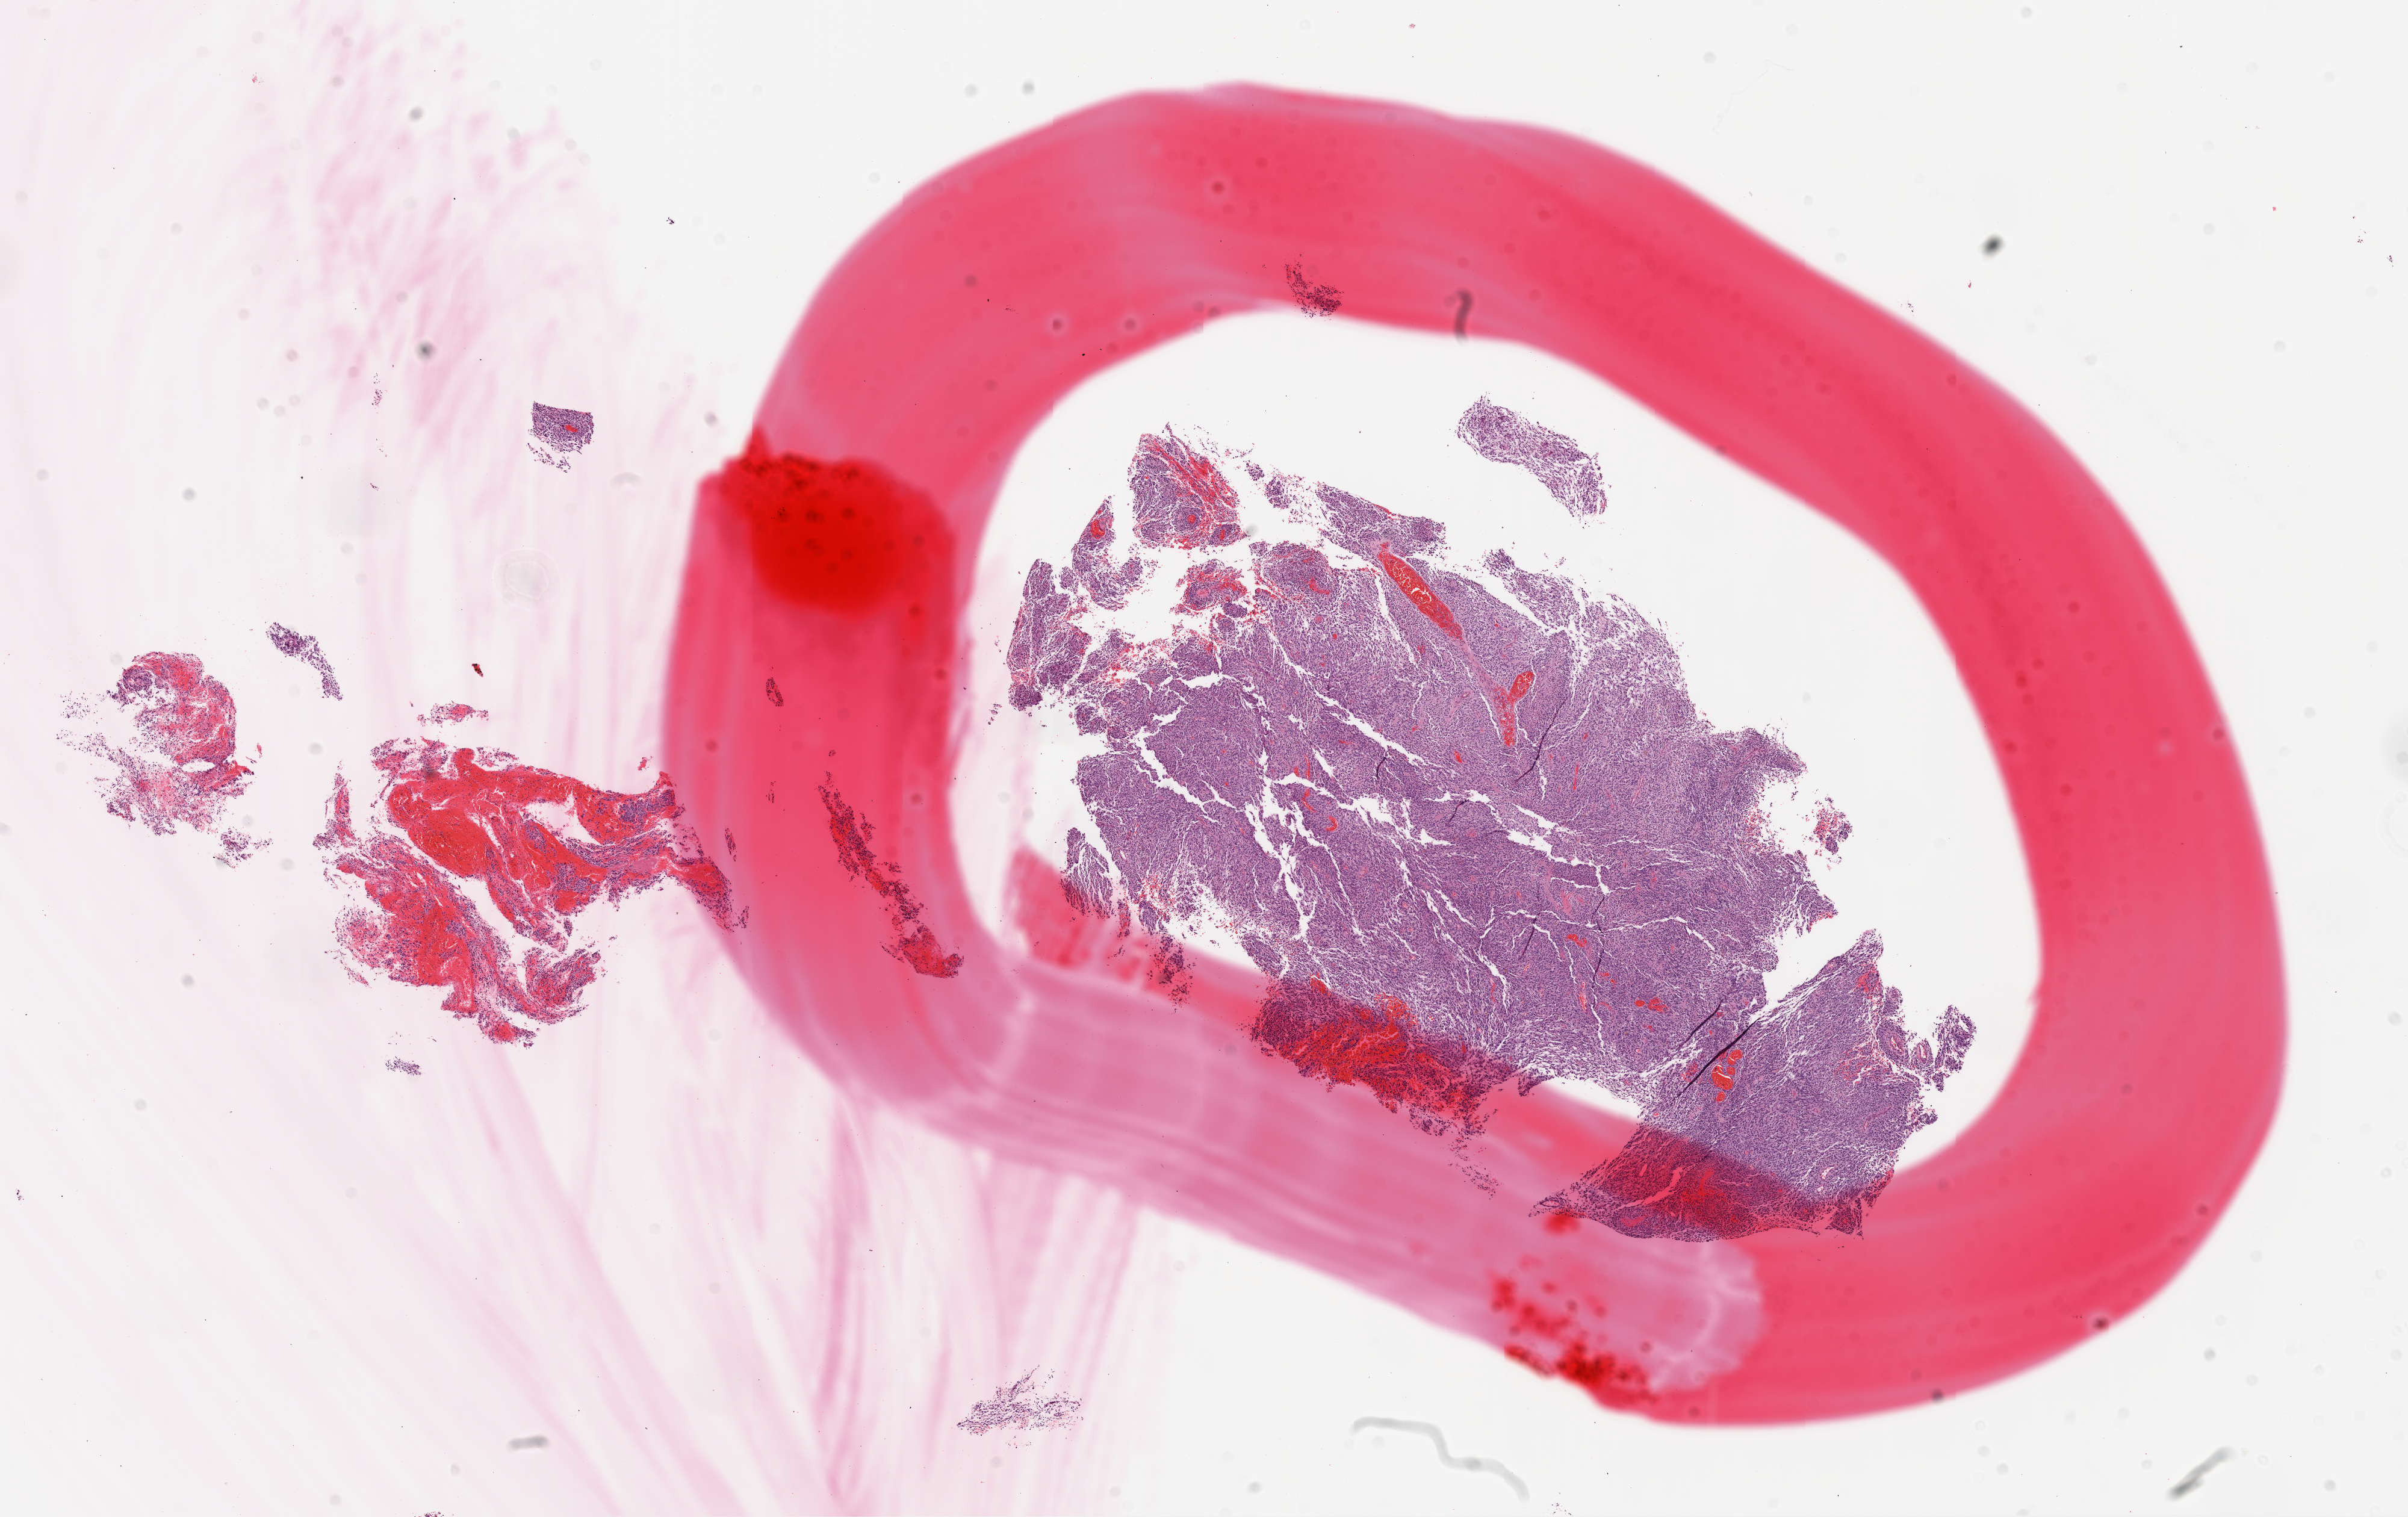
Whole-slide histology image, Hematoxylin and eosin (H&E) stained, a low-resolution overview of the entire scanned area, about 16.0 x 10.1 mm; formalin-fixed paraffin-embedded (FFPE) diagnostic section; primary tumour sample from the brain. Male patient; age at initial diagnosis 61 years.
Histologic diagnosis: Glioblastoma.